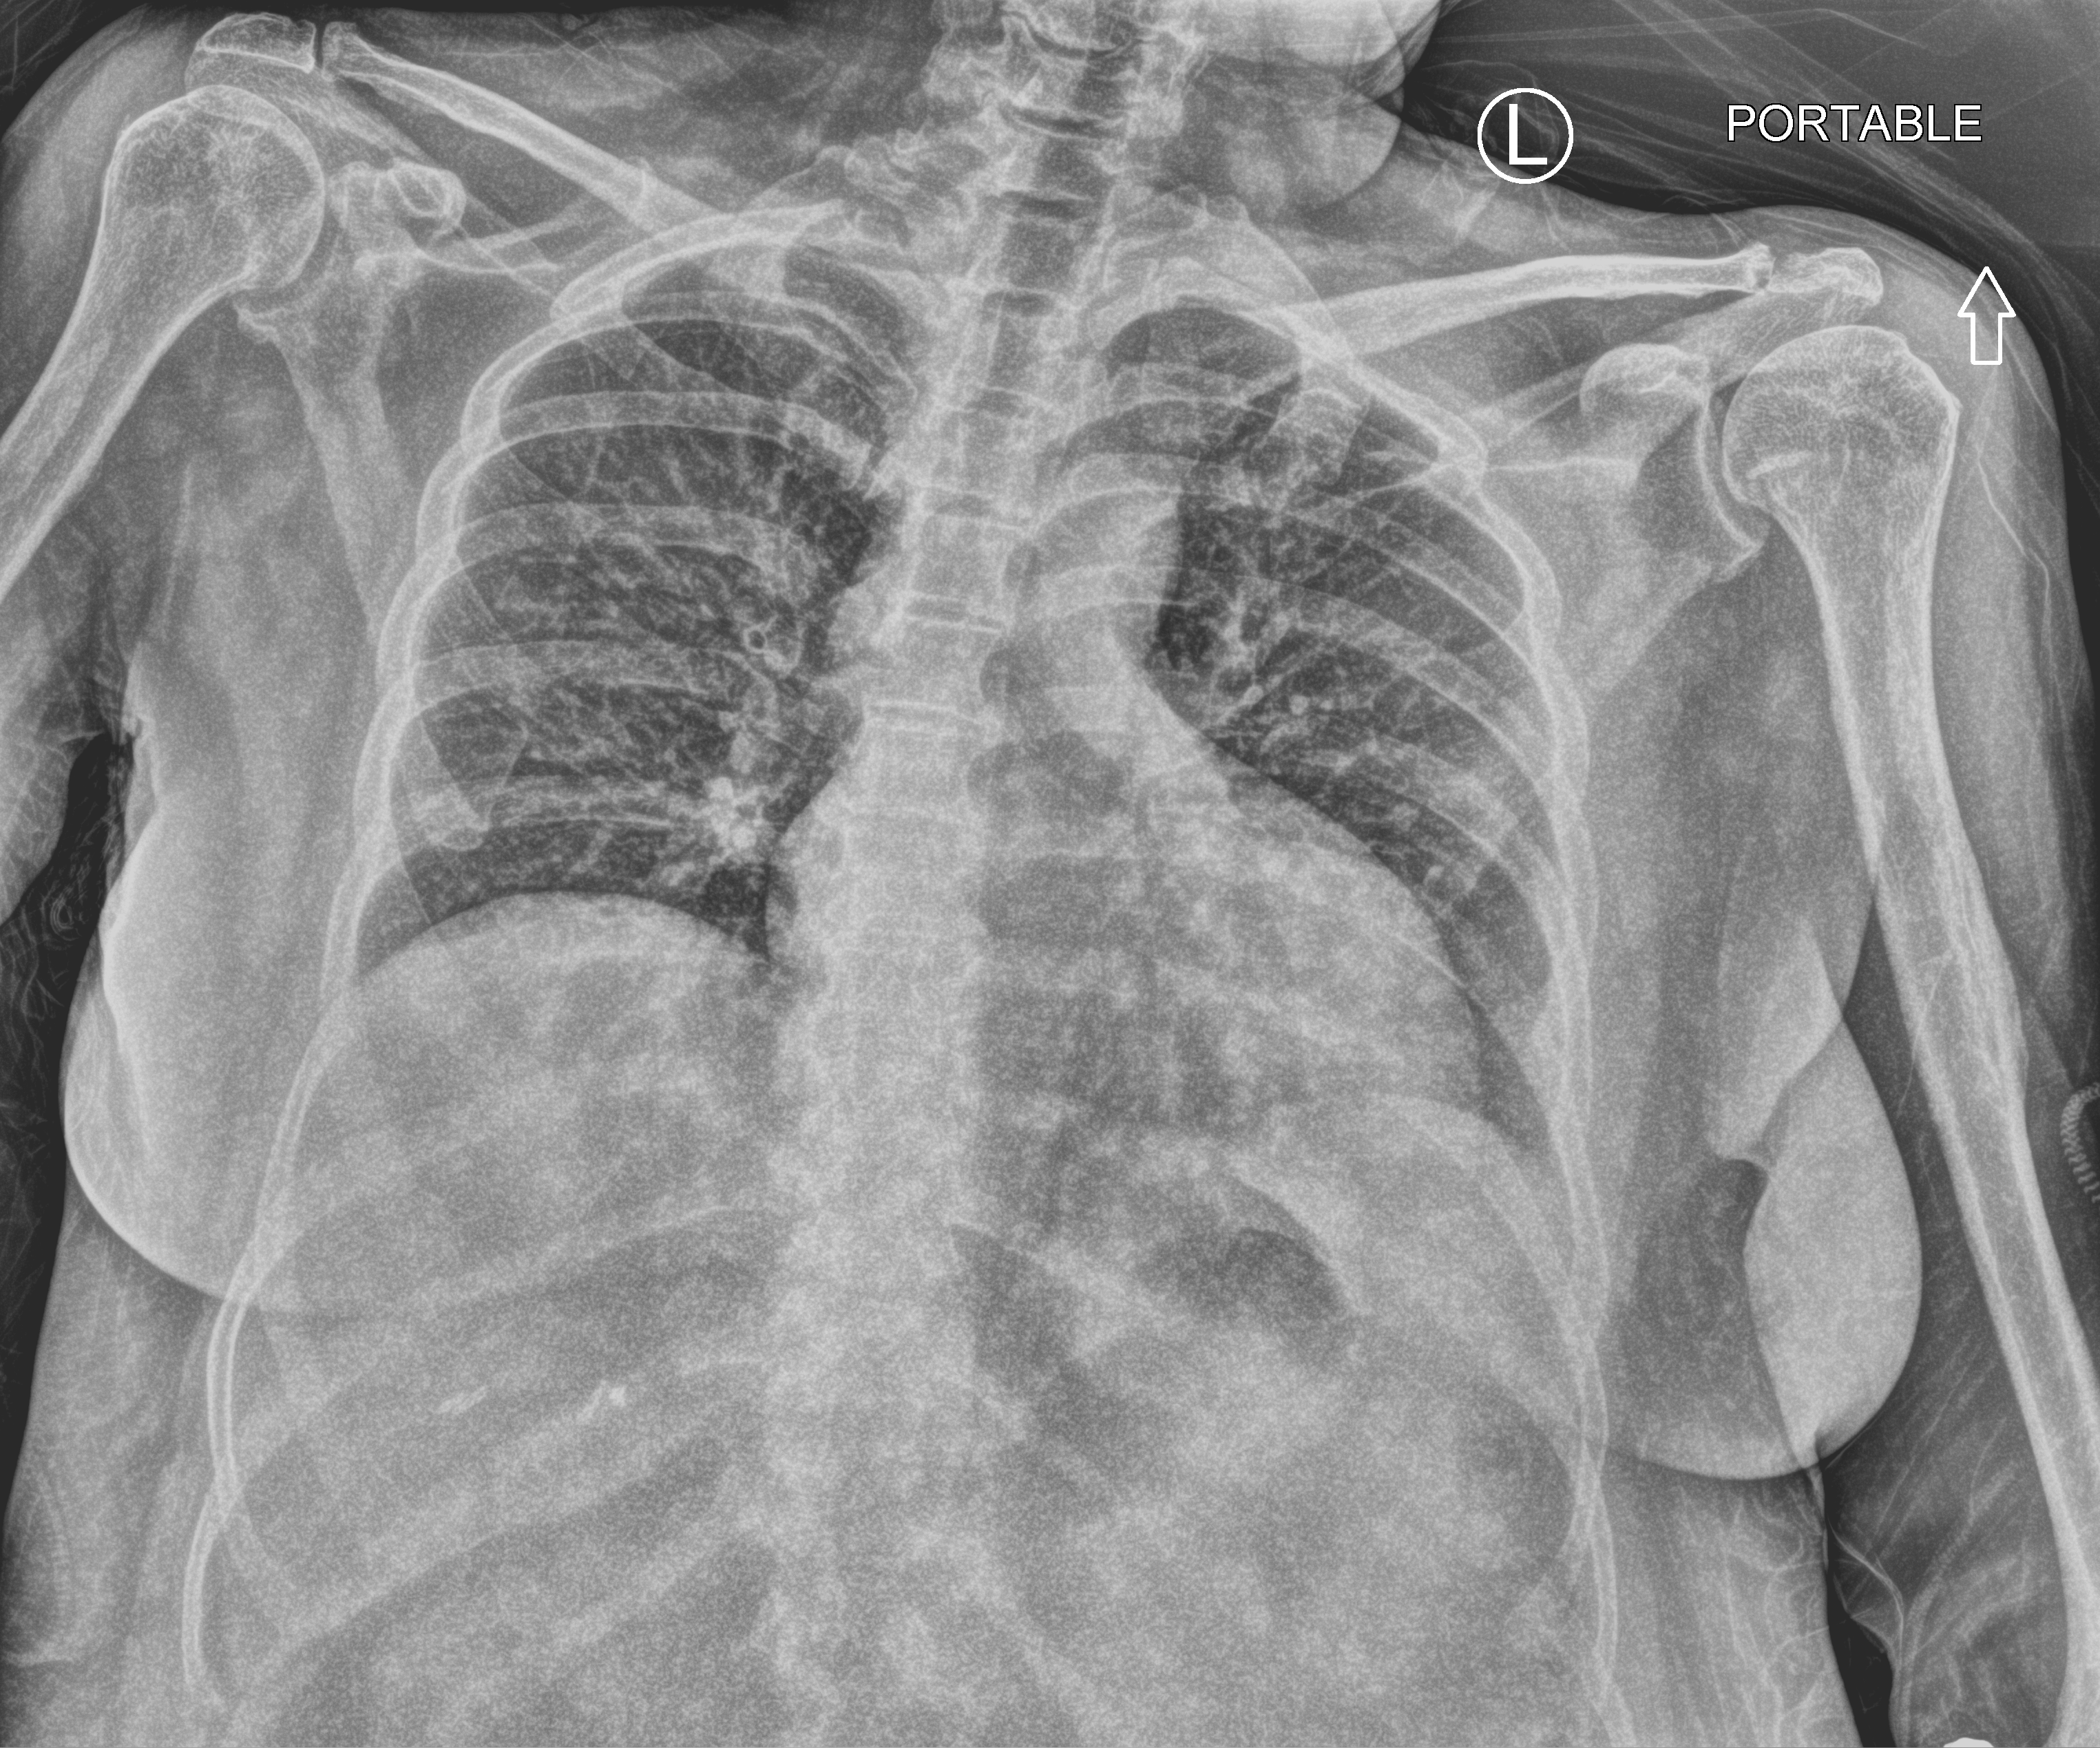
Portable chest radiograph; anteroposterior (AP) projection. Patient hospitalised with COVID-19; female, aged 18–59 years.
Hospital-stay facts (about this admission, not read from this image; timing relative to this image not recorded): mechanically ventilated during this hospital stay: no.